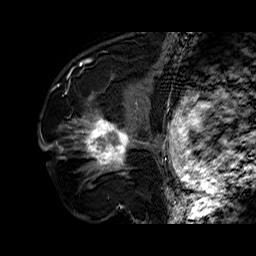
Breast MRI (dynamic contrast-enhanced), one sagittal slice. Position 40 of 60 along the scan axis. Dynamic contrast-enhanced series, time point 2 of 6 at this slice position (early post-contrast). 1.5 T. TE 6.4 ms, TR 32.7 ms. 256 × 256 image matrix, field of view 200 × 200 mm. Female patient. From the clinical record (not read from this slice): setting: breast cancer imaged before/during neoadjuvant chemotherapy; receptor status: HR-positive, HER2-negative.
Structures marked on this image (semi-automatic segmentation, software-assisted and operator-edited):
- analysis volume of interest (the breast-tissue region the enhancement analysis was run in; not a lesion): box from (x=73, y=110) to (x=141, y=179) px
- tumour enhancement mask (voxels above the 100 % enhancement threshold inside the analysis volume of interest): (x=83, y=117)–(x=131, y=168)